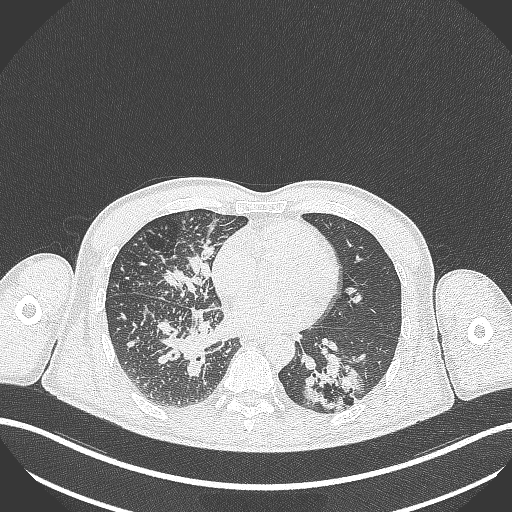
Chest CT, one axial slice. Slice 130 of 348 in the series (ordered by position). Reconstruction kernel B70f. Lung window (W 1500 / L -600 HU). 1 mm slice thickness. 512 × 512 image matrix, field of view 400 × 400 mm. Male patient, age 49 years. From the clinical record (not read from this slice): clinical TNM (as recorded): T2b N1 M0.
Structures marked on this image (rectangle marked by the reading radiologist):
- lung tumour (recorded histology: adenocarcinoma): box from (x=302, y=352) to (x=365, y=410) px